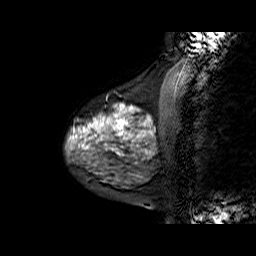
Breast MRI (dynamic contrast-enhanced), one sagittal slice; position 18 of 60 along the scan axis; dynamic contrast-enhanced series, time point 2 of 6 at this slice position (early post-contrast); 1.5 T; TE 6.3 ms, TR 32.9 ms; 4 mm slice thickness; 256 × 256 image matrix, field of view 200 × 200 mm. Female patient. From the clinical record (not read from this slice): setting: breast cancer imaged before/during neoadjuvant chemotherapy; receptor status: HR-positive, HER2-negative.
Annotated regions visible in this slice (semi-automatically segmented with operator editing):
- analysis volume of interest (the breast-tissue region the enhancement analysis was run in; not a lesion): box from (x=68, y=86) to (x=169, y=170) px
- tumour enhancement mask (voxels above the 100 % enhancement threshold inside the analysis volume of interest): (x=70, y=105)–(x=152, y=155)